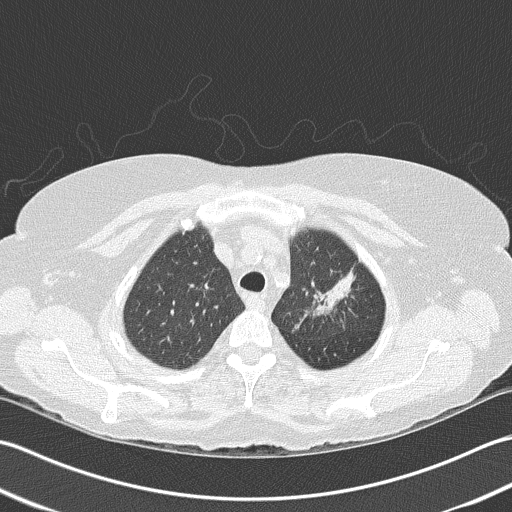
Low-dose screening chest CT, axial slice. First (baseline) screen. Lung window (W 1500 / L -600 HU). Lung (sharp) reconstruction kernel (B50f). Female participant, aged 68 years at enrolment. Former smoker at enrolment.
Expert-annotated lung lesion, bounding box [x1, y1, x2, y2] px = [293, 251, 367, 326]. No non-calcified nodule or mass ≥4 mm was recorded by the screening reader at this exam. Official screen result: negative screen, minor abnormalities not suspicious for lung cancer. Lung cancer was diagnosed 763 days after this screen: adenocarcinoma, NOS, left upper lobe, poorly differentiated (G3), stage IB (AJCC 6th edition), 50 mm at pathology.